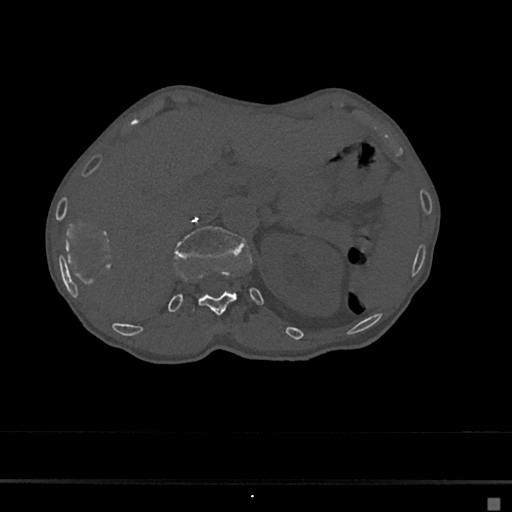
CT including the spine, one axial slice; slice 113 of 797 in the series (ordered by position); reconstruction kernel Br40s/3; 120 kVp; bone window (W 1800 / L 400 HU); 0.5 mm slice thickness; 512 × 512 image matrix, field of view 360 × 360 mm. Female patient, age 68 years. Case-level facts recorded for this patient, not image findings: primary cancer: renal.
Structures marked on this image (semi-automatically segmented with operator editing):
- L1 vertebra: bounding box (x1, y1, x2, y2) in pixels: (174, 226, 248, 257)
- T12 vertebra: (192, 267, 243, 315)